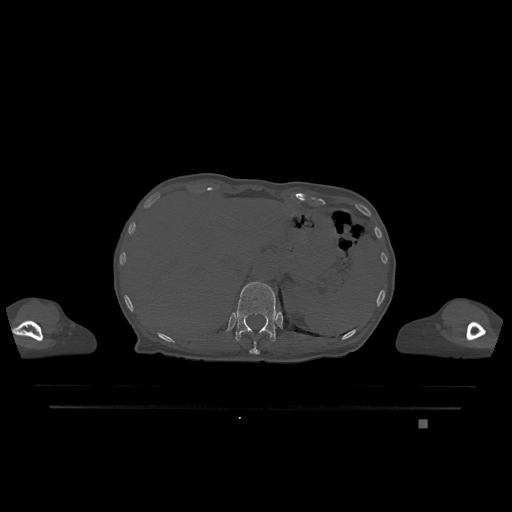
CT including the spine, one axial slice. Slice 547 of 1317 in the series (ordered by position). Bone window (W 1800 / L 400 HU). 0.5 mm slice thickness. 512 × 512 image matrix, field of view 500 × 500 mm. Patient: female, 74 years. Case-level facts recorded for this patient, not image findings: primary cancer: lung.
Structures marked on this image (semi-automatically segmented with operator editing):
- T11 vertebra: box from (x=249, y=342) to (x=260, y=355) px
- T12 vertebra: (x=235, y=282)–(x=278, y=342)